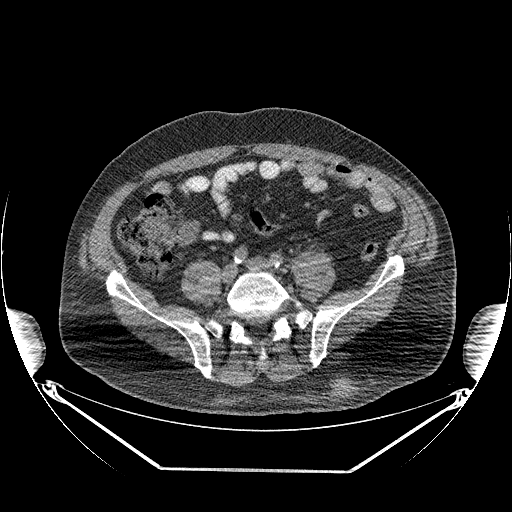
CT of an extremity soft-tissue mass (from a PET/CT study), one axial slice; slice 96 of 267 in the series (ordered by position); reconstruction kernel STANDARD; 140 kVp; soft-tissue window (W 400 / L 40 HU); 3.75 mm slice thickness; 512 × 512 image matrix, field of view 500 × 500 mm. Male patient. Case-level facts recorded for this patient, not image findings: histological type: pleiomorphic leiomyosarcoma; grade: high; site of the primary tumour: left buttock.
Annotated regions visible in this slice (expert contour drawn on MRI and transferred to this co-registered scan by the dataset authors):
- gross tumour volume including surrounding oedema: bounding box [x1, y1, x2, y2] px = [329, 377, 348, 403]
- gross tumour volume (mass): [331, 381, 348, 401]